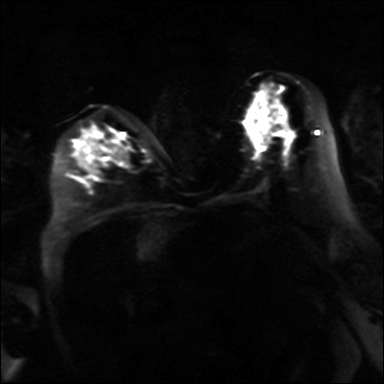
Breast MRI, one axial slice; position 16 of 36 along the scan axis; diffusion-weighted series; image 2 of 4 stored at this slice position (different b-values; order by instance number); 3 T; 384 × 384 image matrix. Female patient.
Outlined on this slice (outlined manually by an expert reader):
- tumour on diffusion-weighted imaging: box from (x=258, y=103) to (x=274, y=132) px